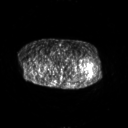
FDG PET of an extremity soft-tissue mass (from a PET/CT study), one axial slice; position 256 of 267 along the scan axis; 3.27 mm slice thickness; 128 × 128 image matrix, field of view 700 × 700 mm. Patient: female, 62 years. From the clinical record (not read from this slice): histological type: undifferentiated – high grade; grade: high; site of the primary tumour: left thigh.
Annotated regions visible in this slice (expert contour drawn on MRI and transferred to this co-registered scan by the dataset authors):
- gross tumour volume including surrounding oedema: bounding box [x1, y1, x2, y2] px = [86, 67, 94, 78]
- gross tumour volume (mass): [88, 73, 92, 76]